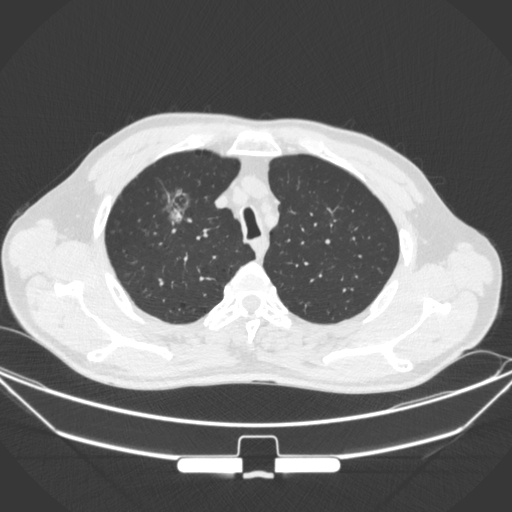
Chest CT, one axial slice. Slice 280 of 355 in the series (ordered by position). 120 kVp. Lung window (W 1500 / L -600 HU). 512 × 512 image matrix, field of view 399 × 399 mm. Patient: male, 67 years. Case-level facts recorded for this patient, not image findings: clinical TNM (as recorded): T1c N0 M0.
Annotated regions visible in this slice (bounding box drawn by a radiologist):
- lung tumour (recorded histology: adenocarcinoma): box from (x=142, y=175) to (x=196, y=230) px